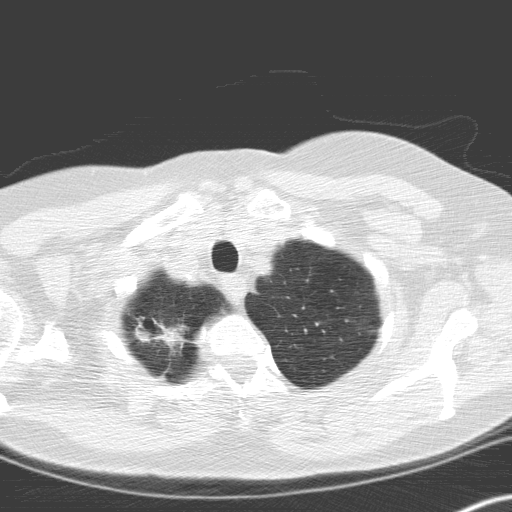
Low-dose screening chest CT, one axial slice. Slice 143 of 166 in the series (ordered by position). 120 kVp. Lung window (W 1500 / L -600 HU). 512 × 512 image matrix.
Structures marked on this image (expert manual segmentation):
- lesion 1 (tumor, upper lobe of right lung): bounding box (x1, y1, x2, y2) in pixels: (162, 326, 184, 348)